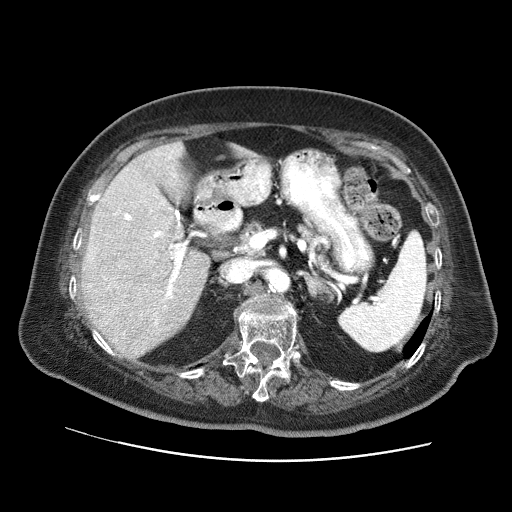
Contrast-enhanced abdominal CT (liver protocol), one axial slice. Position 37 of 73 along the scan axis. Soft-tissue window (W 400 / L 40 HU). 2.5 mm slice thickness. 512 × 512 image matrix, field of view 380 × 380 mm. Case-level facts recorded for this patient, not image findings: diagnosis: hepatocellular carcinoma (patient treated with transarterial chemoembolisation; whether this scan precedes or follows treatment is not stated here); TNM stage (as recorded): Stage-I; Child-Pugh class: A; tumour differentiation: well differentiated; tumour nodularity: uninodular.
Outlined on this slice (semi-automatically segmented with operator editing):
- liver parenchyma outside the tumour (the mass and vessels are separate outlines, so this box may not span the whole liver): bounding box [x1, y1, x2, y2] px = [82, 142, 210, 356]
- liver vessels: [124, 151, 182, 325]